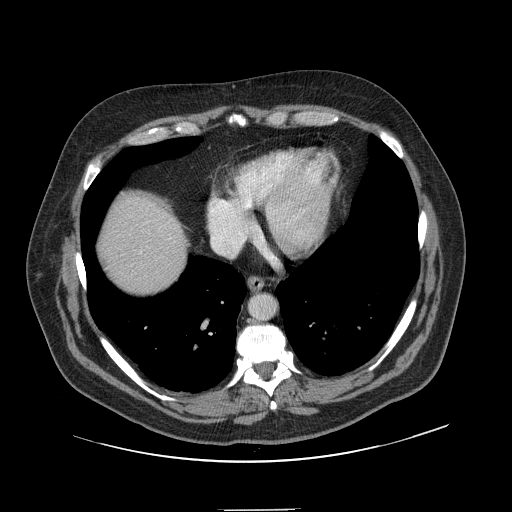
Contrast-enhanced abdominal CT, one axial slice; slice 139 of 154 in the series (ordered by position); intravenous contrast given; soft-tissue window (W 400 / L 40 HU); 512 × 512 image matrix, field of view 451 × 451 mm. Male patient, age 61 years. From the clinical record (not read from this slice): diagnosis: colorectal cancer liver metastases, imaged before liver resection; multiple liver metastases: yes; largest metastasis: 2.6 cm.
Structures marked on this image (manually delineated by an expert):
- liver: bounding box (x1, y1, x2, y2) in pixels: (100, 194, 186, 296)
- planned liver remnant (the part of the liver to remain after resection): (99, 194, 186, 296)